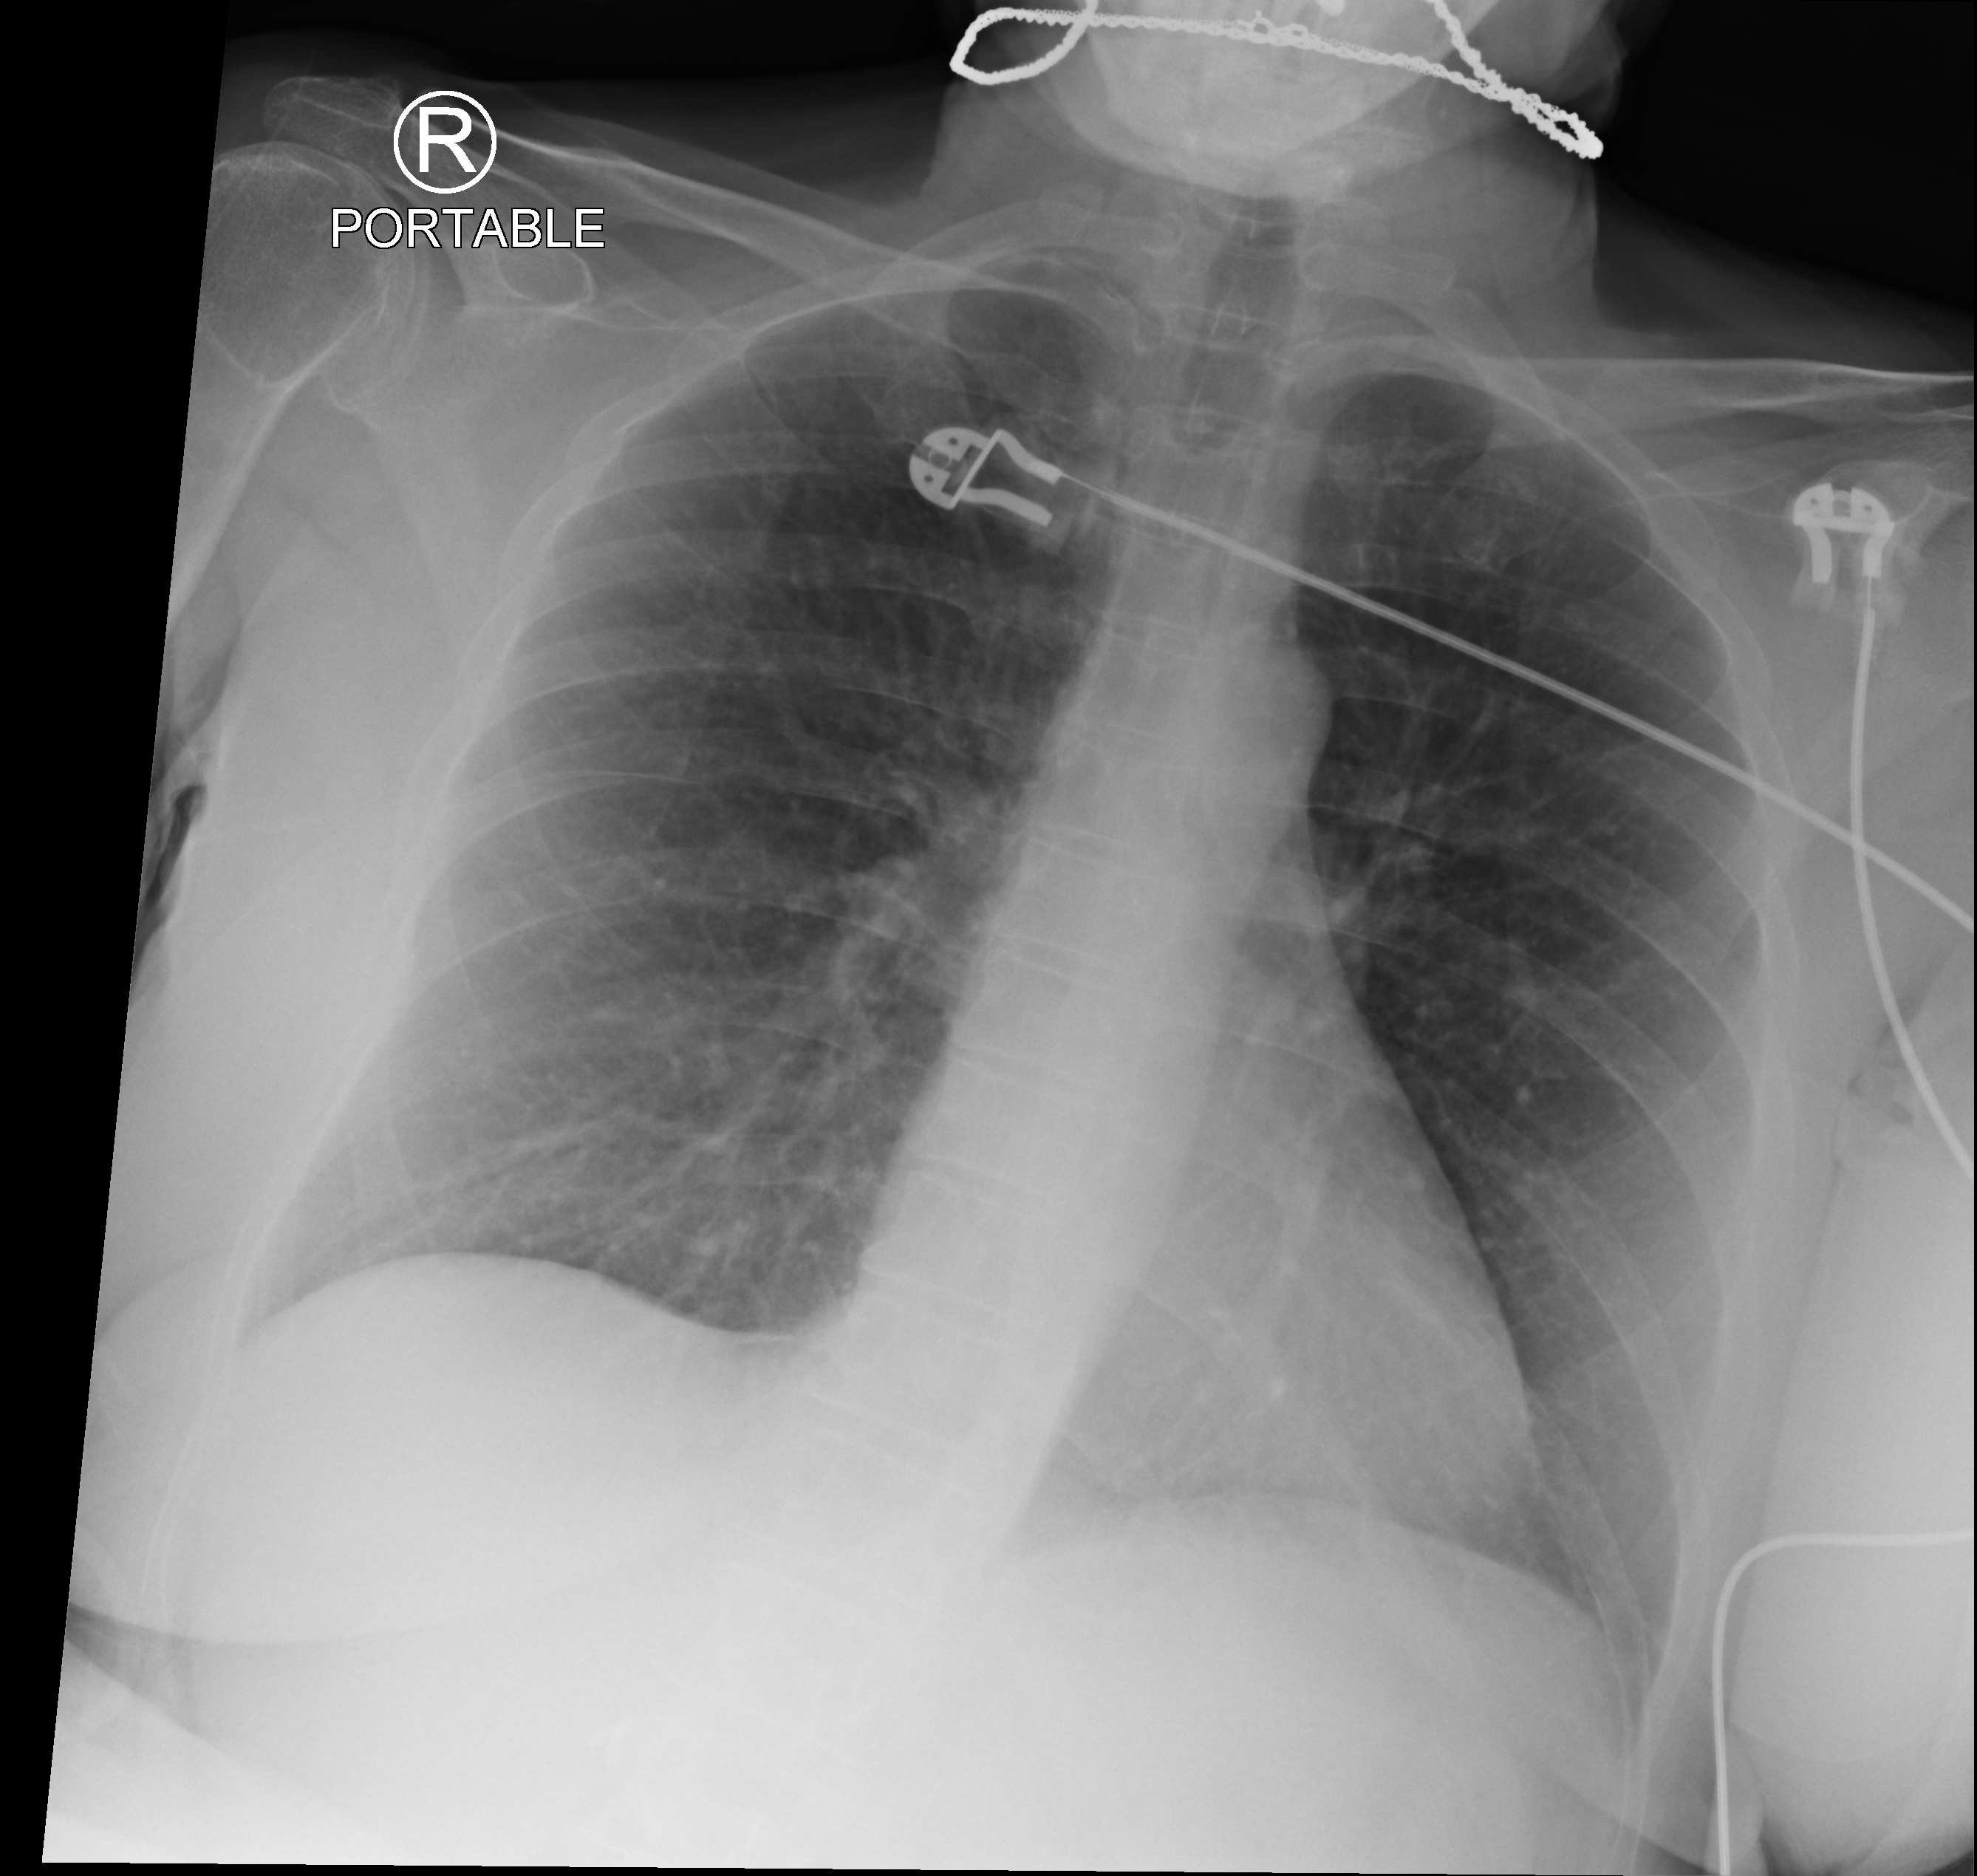
Portable chest radiograph; anteroposterior (AP) projection. Patient hospitalised with COVID-19; female, aged 60–74 years.
Hospital-stay facts (about this admission, not read from this image; timing relative to this image not recorded): mechanically ventilated during this hospital stay: no.